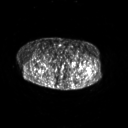
FDG PET of an extremity soft-tissue mass (from a PET/CT study), one axial slice; position 261 of 267 along the scan axis; 3.27 mm slice thickness; 128 × 128 image matrix, field of view 700 × 700 mm. Patient: female, 62 years. Case-level facts recorded for this patient, not image findings: histological type: undifferentiated – high grade; grade: high; site of the primary tumour: left thigh.
Structures marked on this image (expert contour drawn on MRI and transferred to this co-registered scan by the dataset authors):
- gross tumour volume including surrounding oedema: bounding box [x1, y1, x2, y2] px = [89, 72, 92, 75]